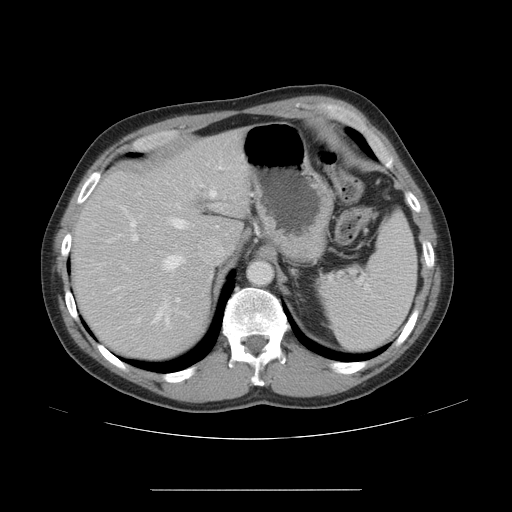
Contrast-enhanced abdominal CT, one axial slice. Position 34 of 48 along the scan axis. Reconstruction kernel STANDARD. Soft-tissue window (W 400 / L 40 HU). 5 mm slice thickness. 512 × 512 image matrix. Male patient, age 56 years. Case-level facts recorded for this patient, not image findings: diagnosis: colorectal cancer liver metastases, imaged before liver resection; multiple liver metastases: yes; largest metastasis: 1.8 cm; disease in both lobes: yes.
Annotated regions visible in this slice (manually delineated by an expert):
- hepatic veins: bounding box (x1, y1, x2, y2) in pixels: (136, 191, 218, 328)
- liver: (77, 136, 247, 356)
- planned liver remnant (the part of the liver to remain after resection): (78, 136, 247, 356)
- portal vein (with intrahepatic branches): (120, 160, 221, 302)